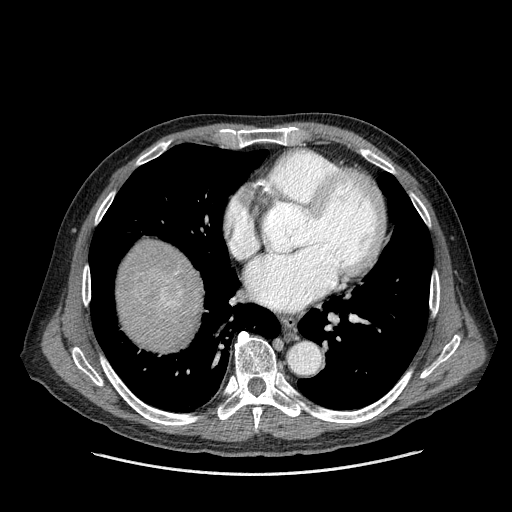
Contrast-enhanced abdominal CT (liver protocol), one axial slice. Slice 158 of 180 in the series (ordered by position). Reconstruction kernel STANDARD. One of 2 acquisitions stored at this slice position. Soft-tissue window (W 400 / L 40 HU). 2.5 mm slice thickness. 512 × 512 image matrix, field of view 420 × 420 mm. Case-level facts recorded for this patient, not image findings: diagnosis: hepatocellular carcinoma (patient treated with transarterial chemoembolisation; whether this scan precedes or follows treatment is not stated here); TNM stage (as recorded): Stage-II; Child-Pugh class: A.
Structures marked on this image (semi-automatically segmented with operator editing):
- liver parenchyma outside the tumour (the mass and vessels are separate outlines, so this box may not span the whole liver): bounding box [x1, y1, x2, y2] px = [118, 240, 202, 352]
- mass: [134, 268, 186, 309]